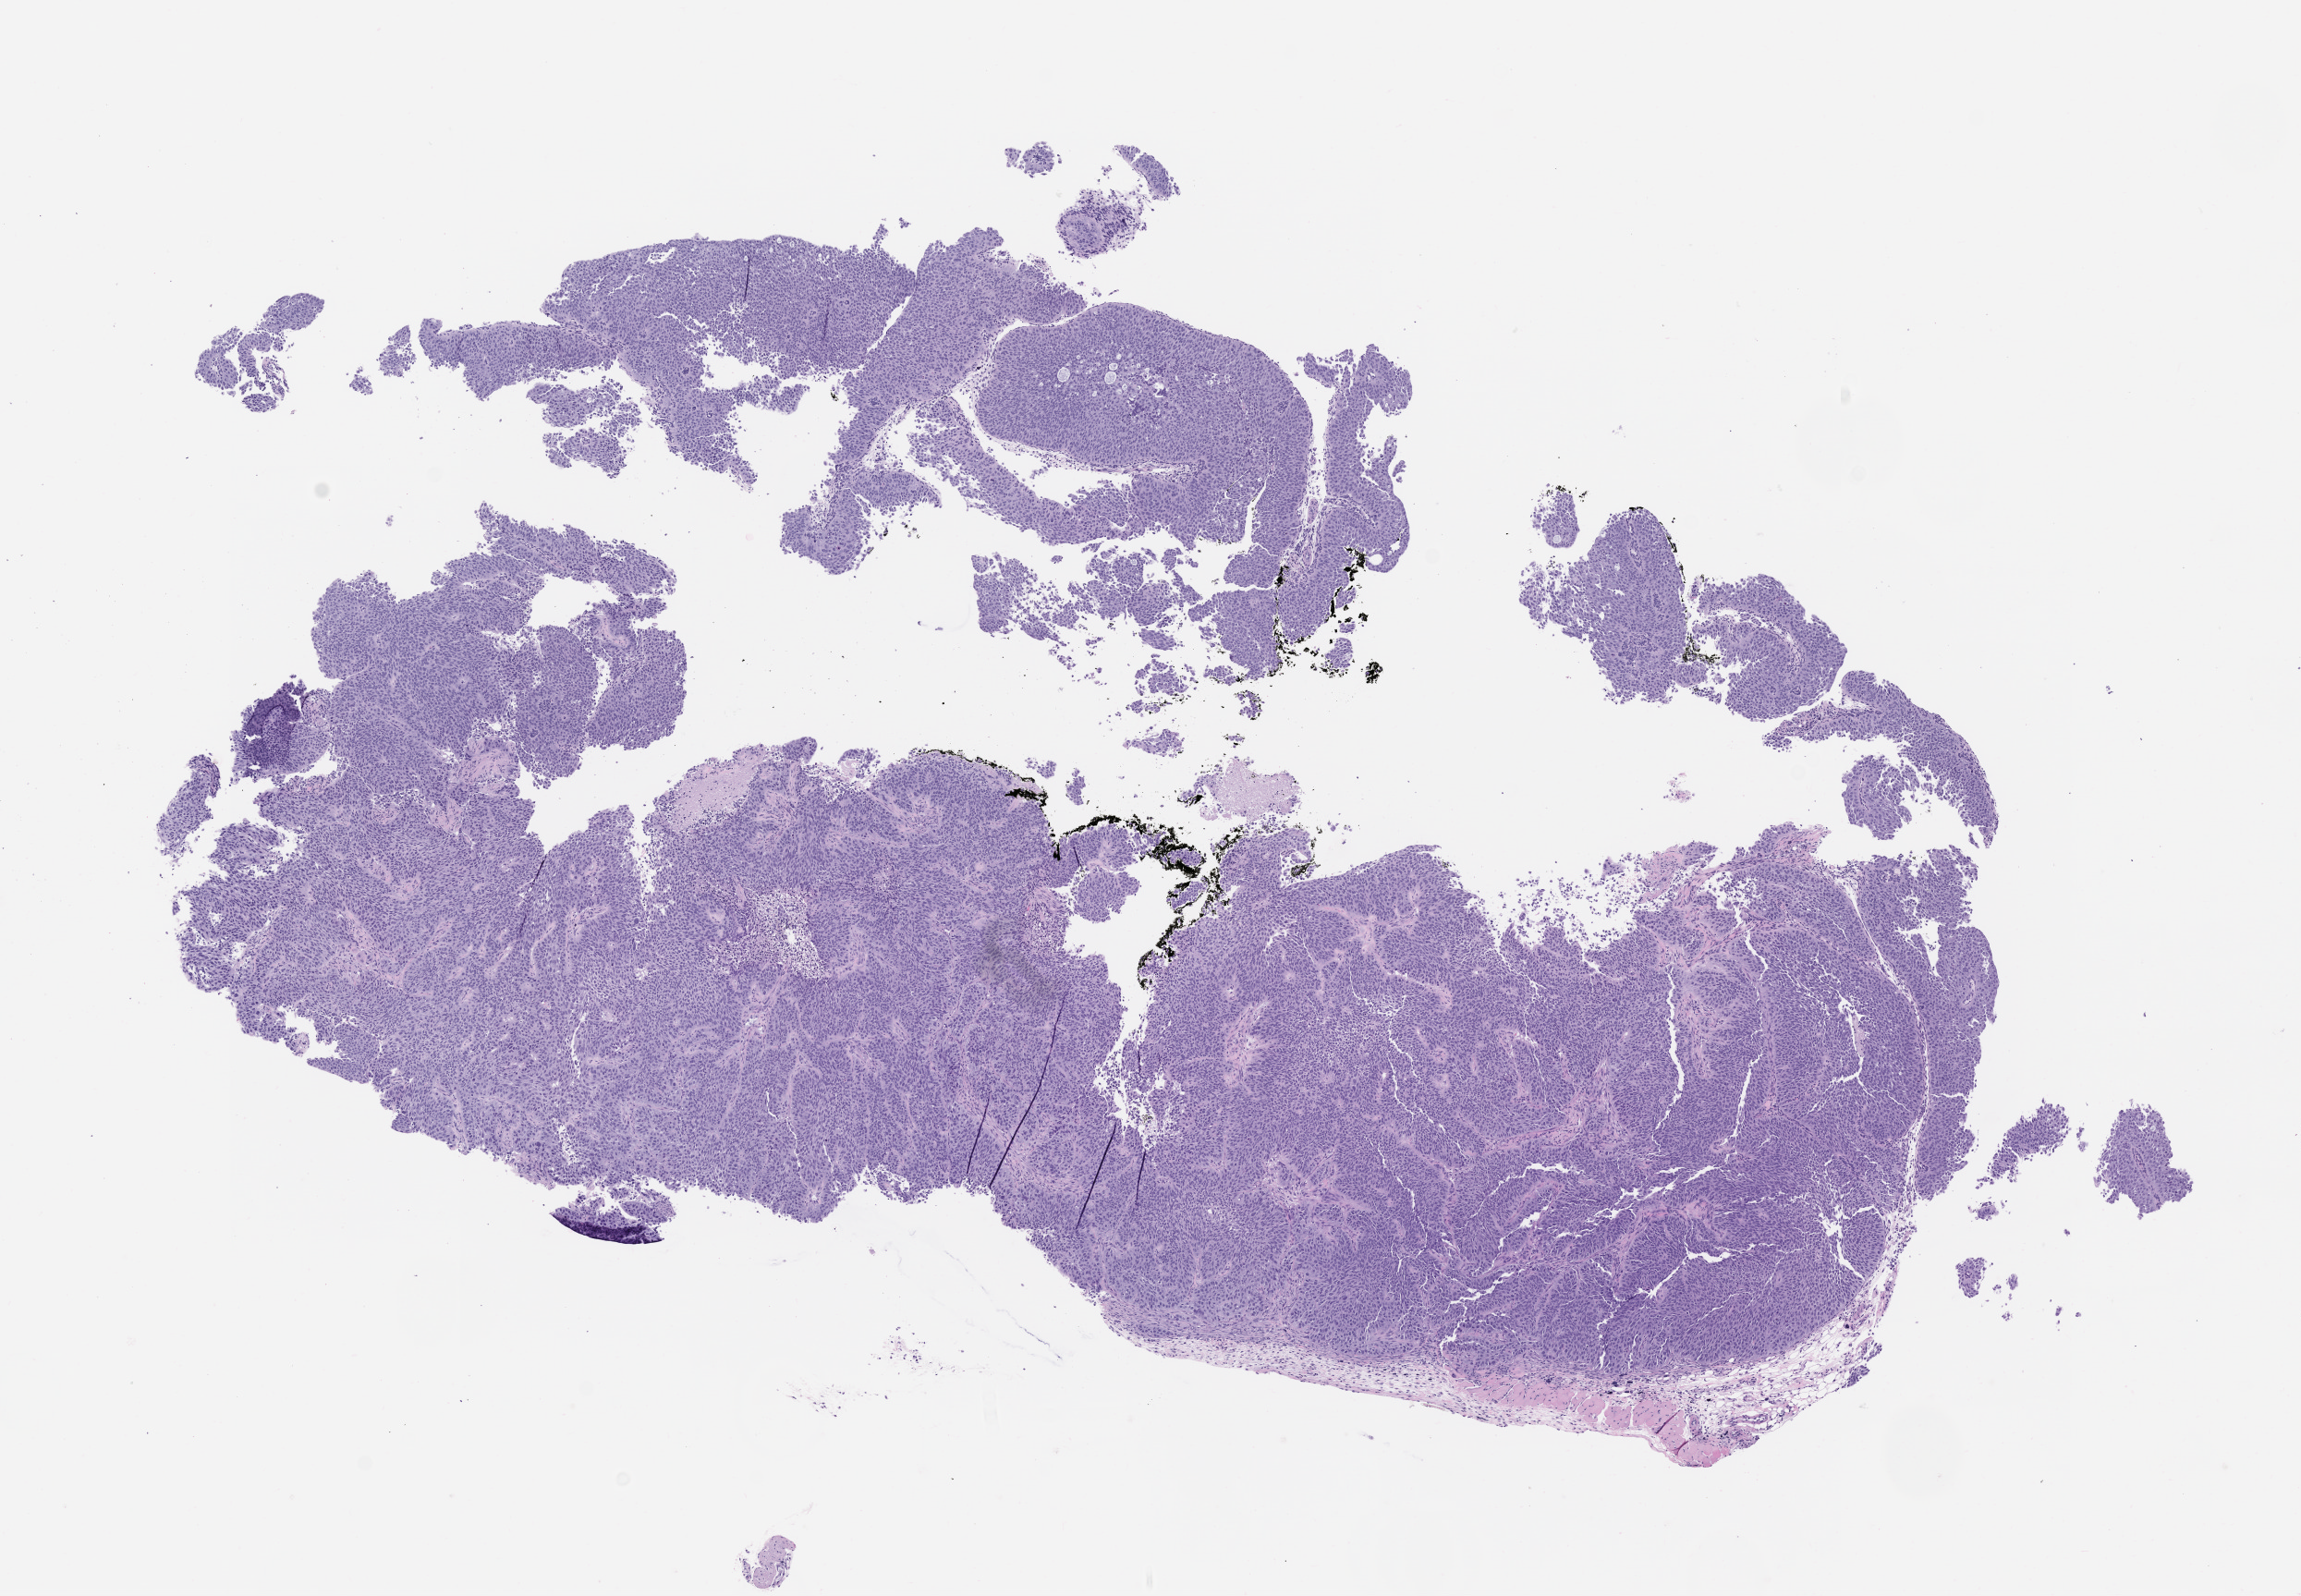
Hematoxylin and eosin (H&E) whole-slide image of a patient-derived xenograft (PDX) tumor grown in a mouse, passage 1, a low-resolution overview of the entire scanned area, about 10.0 x 6.9 mm. Formalin-fixed paraffin-embedded section. Originating tumor site category: lung.
Originating patient diagnosis: Lung Squamous Cell Carcinoma.